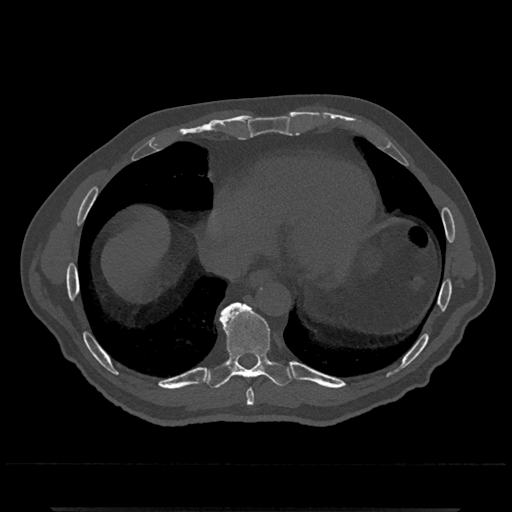
CT including the spine, one axial slice. Slice 622 of 797 in the series (ordered by position). Reconstruction kernel Br40s/3. 120 kVp. Bone window (W 1800 / L 400 HU). 0.5 mm slice thickness. 512 × 512 image matrix. Male patient, age 67 years. From the clinical record (not read from this slice): primary cancer: prostate.
Structures marked on this image (semi-automatically segmented with operator editing):
- T8 vertebra: bounding box (x1, y1, x2, y2) in pixels: (246, 389, 255, 407)
- T9 vertebra: (204, 302, 295, 389)